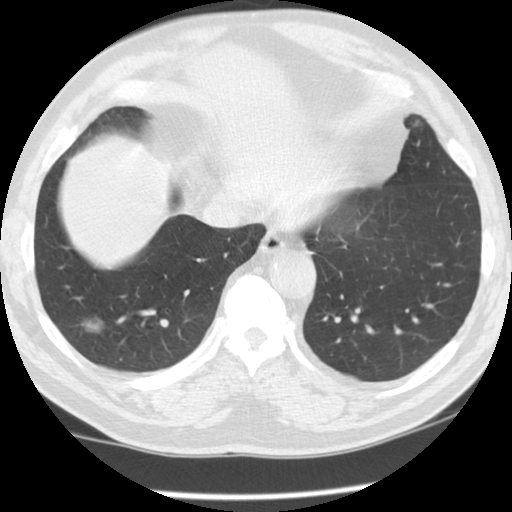
Low-dose screening chest CT, one axial slice; position 29 of 115 along the scan axis; 120 kVp; lung window (W 1500 / L -600 HU); 2.5 mm slice thickness; 512 × 512 image matrix.
Structures marked on this image (outlined manually by an expert reader):
- lesion 1 (tumor, lower lobe of right lung): box from (x=83, y=318) to (x=103, y=333) px